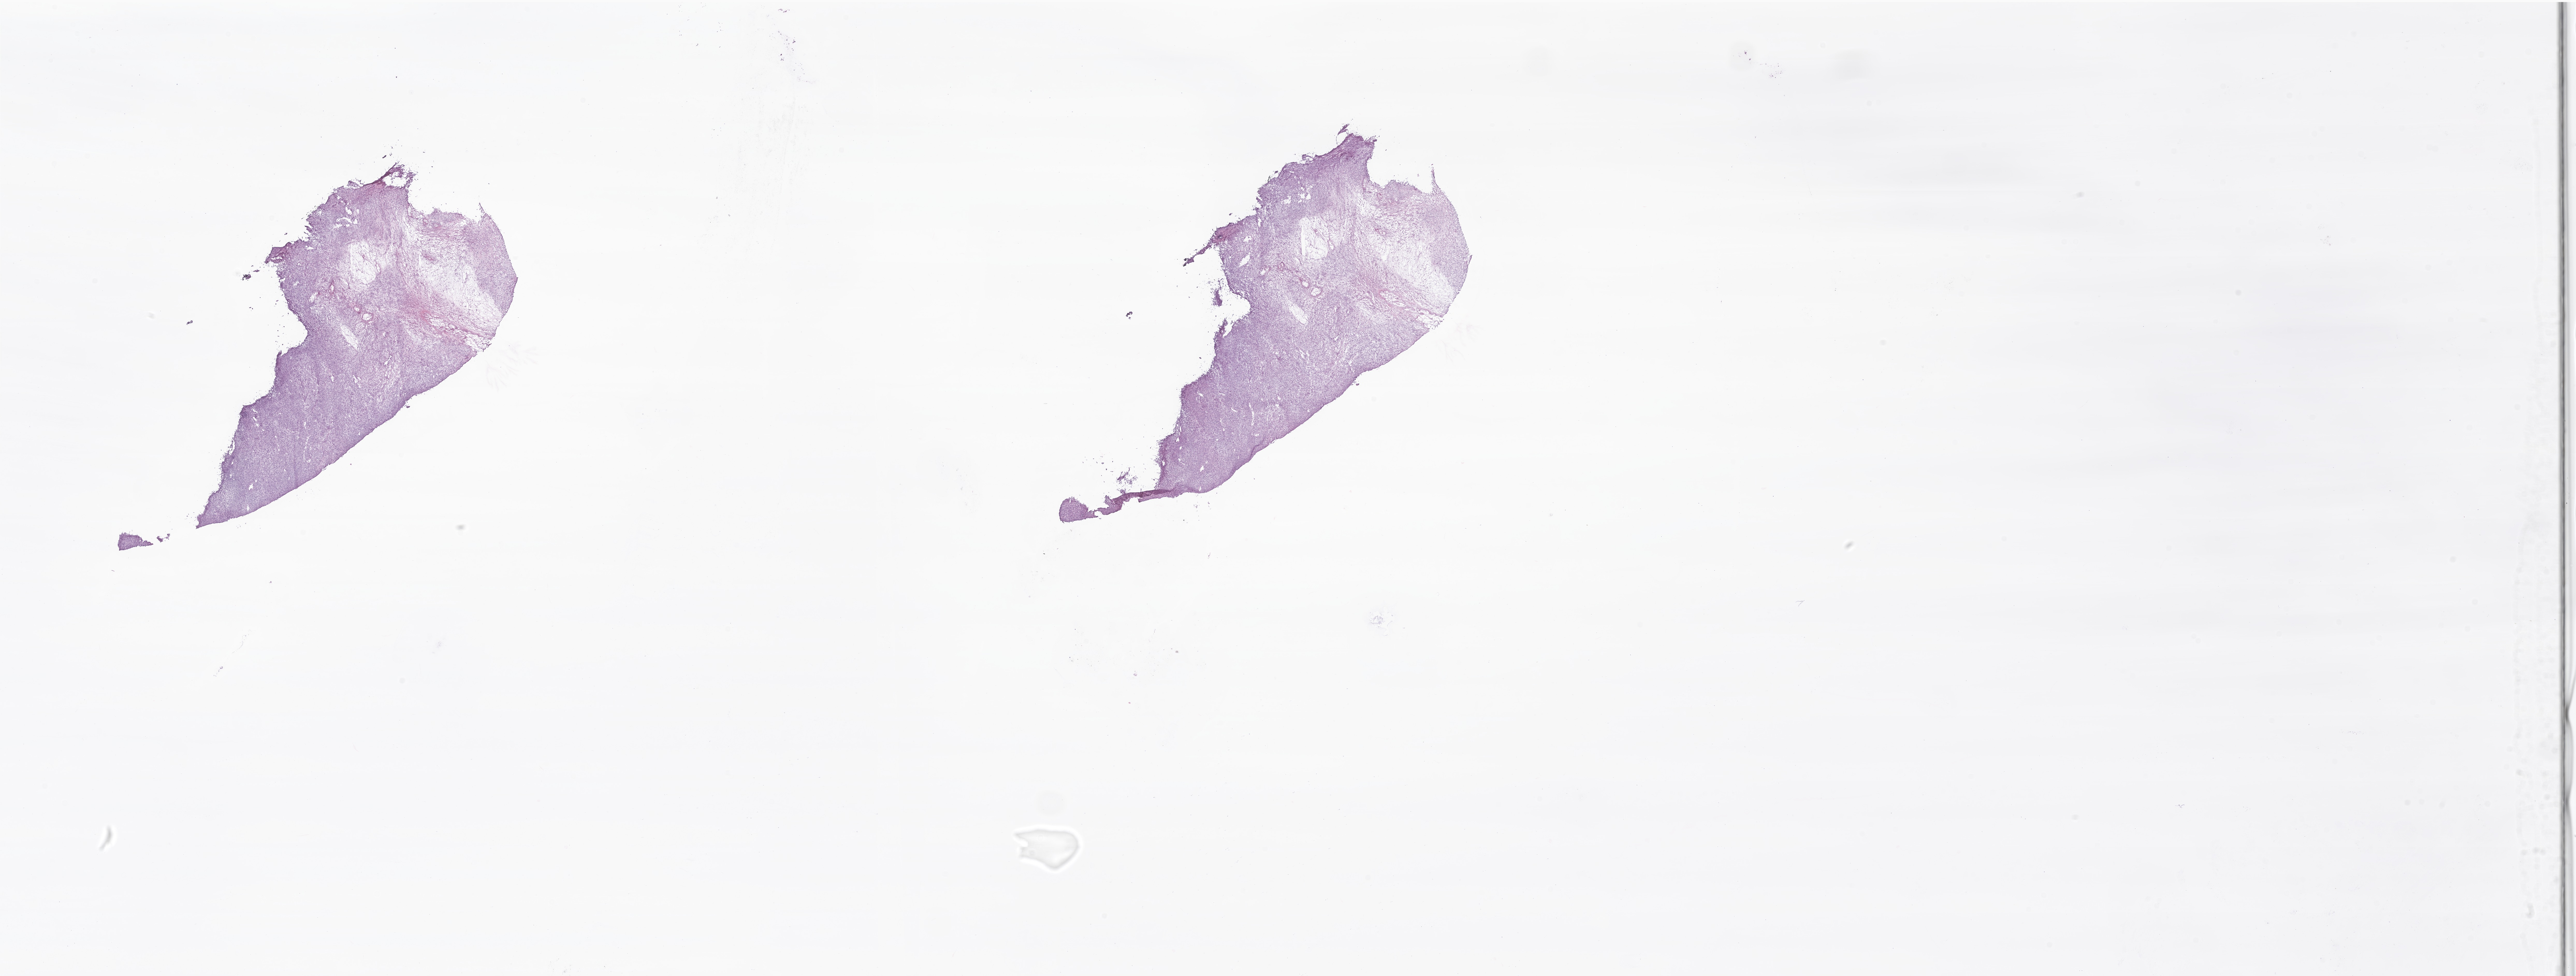
Whole-slide image, hematoxylin and eosin (H&E) stain of tumor tissue from the soft tissue of trunk, a low-resolution overview of the entire scanned area, about 41.9 x 15.9 mm. Frozen section (OCT-embedded). Patient female; age 197 months (16 years 5 months).
Recorded diagnosis: Leiomyosarcoma, NOS.